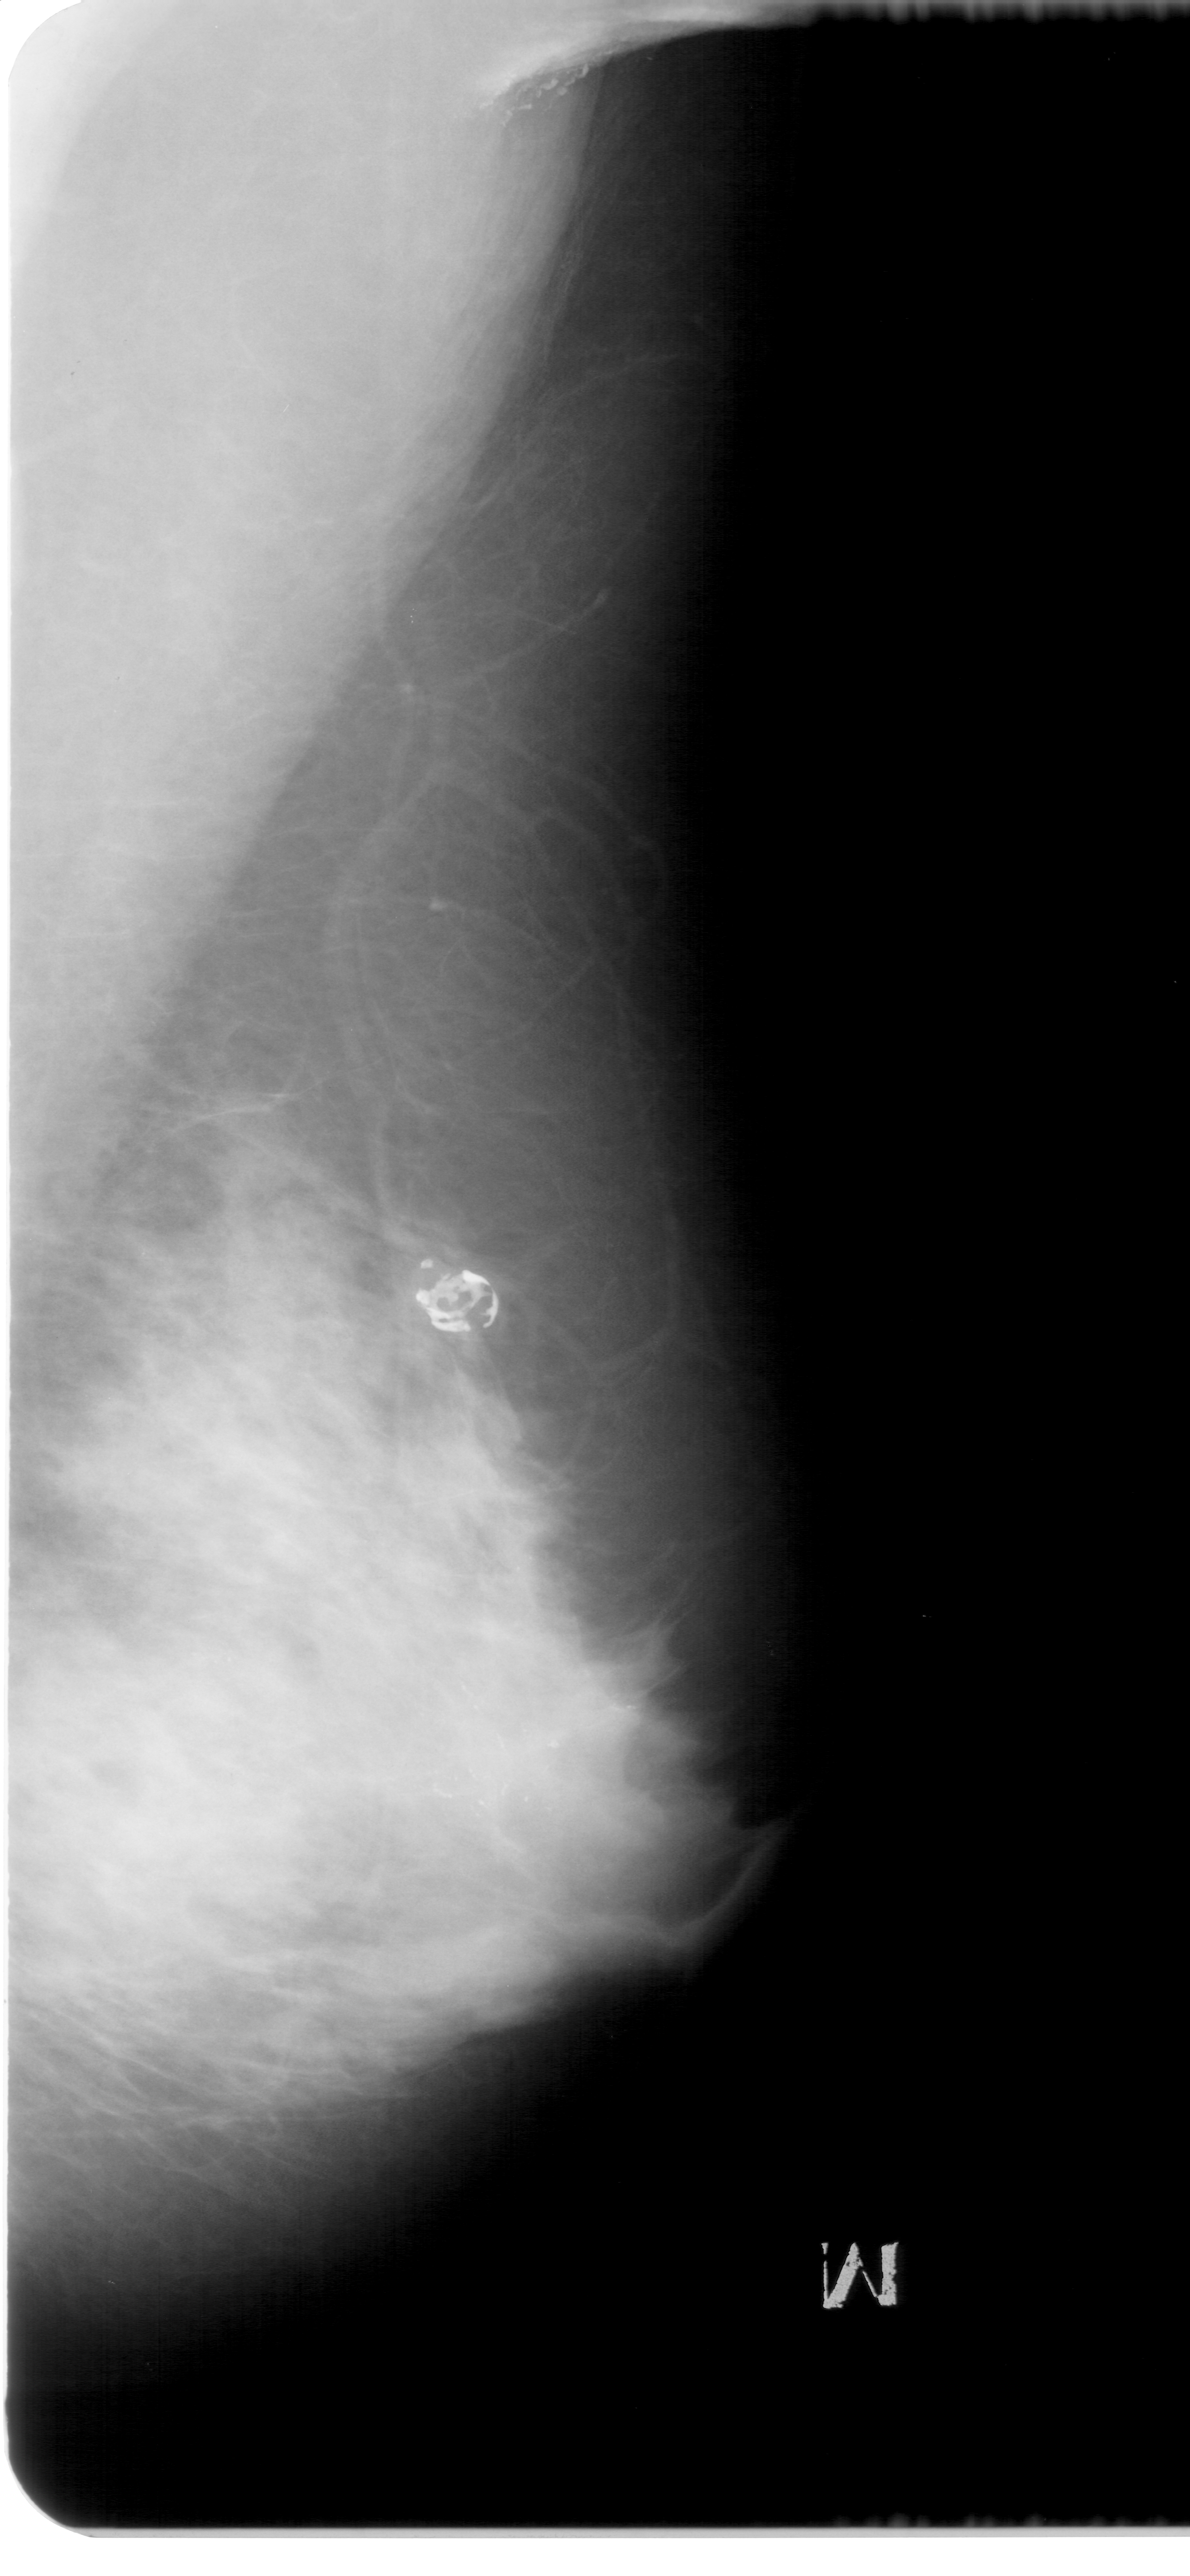
Mammogram (digitized film). Right breast. MLO view. Breast composition: extremely dense (BI-RADS density category 4 of 4). 1190 × 2576 image matrix.
Marked abnormalities (boxes around the expert regions of interest):
- calcifications, morphology pleomorphic, distribution segmental; BI-RADS assessment category 5; subtlety rating 4 on a 1 (subtle) to 5 (obvious) scale; pathology (as recorded): malignant: bounding box <197,1633,658,1862> (left, top, right, bottom; pixels)